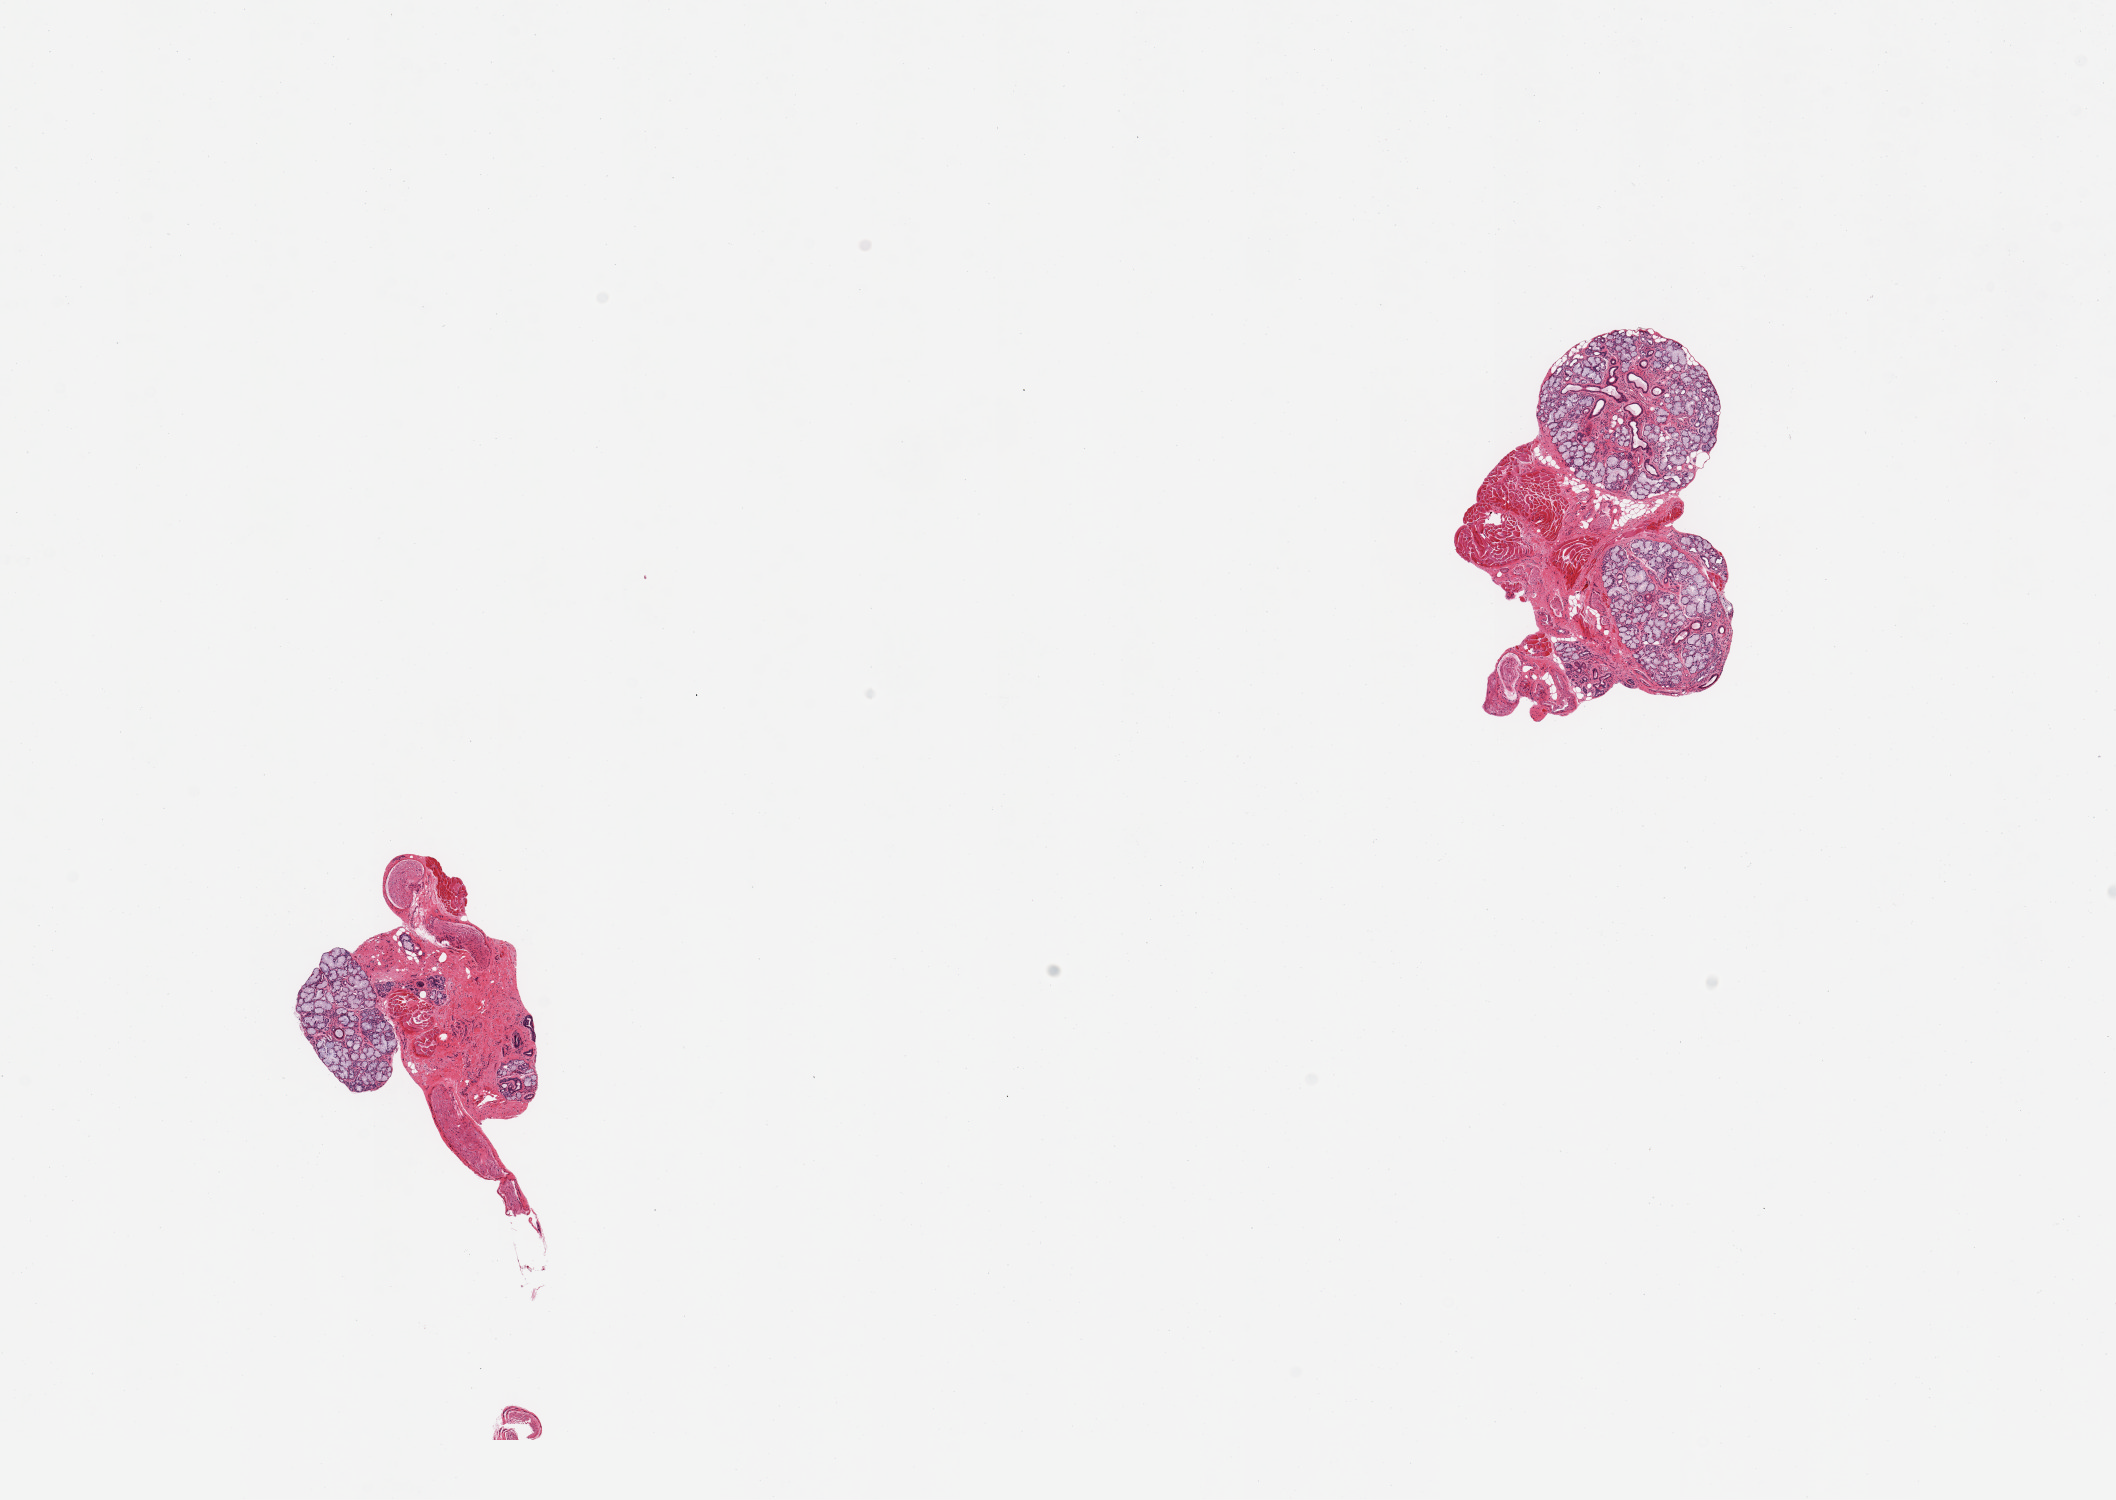
Whole-slide image, haematoxylin and eosin stain — whole scanned area (about 16.7 x 11.9 mm) shown as a low-resolution overview; PAXgene-fixed, paraffin-embedded tissue; target tissue: minor salivary gland; tissue donor sample. Female donor.
Pathologist's review note for this sample: 2 pieces with 3 salivary glands and >50% muscular, vascular, neural and fibrous contents.